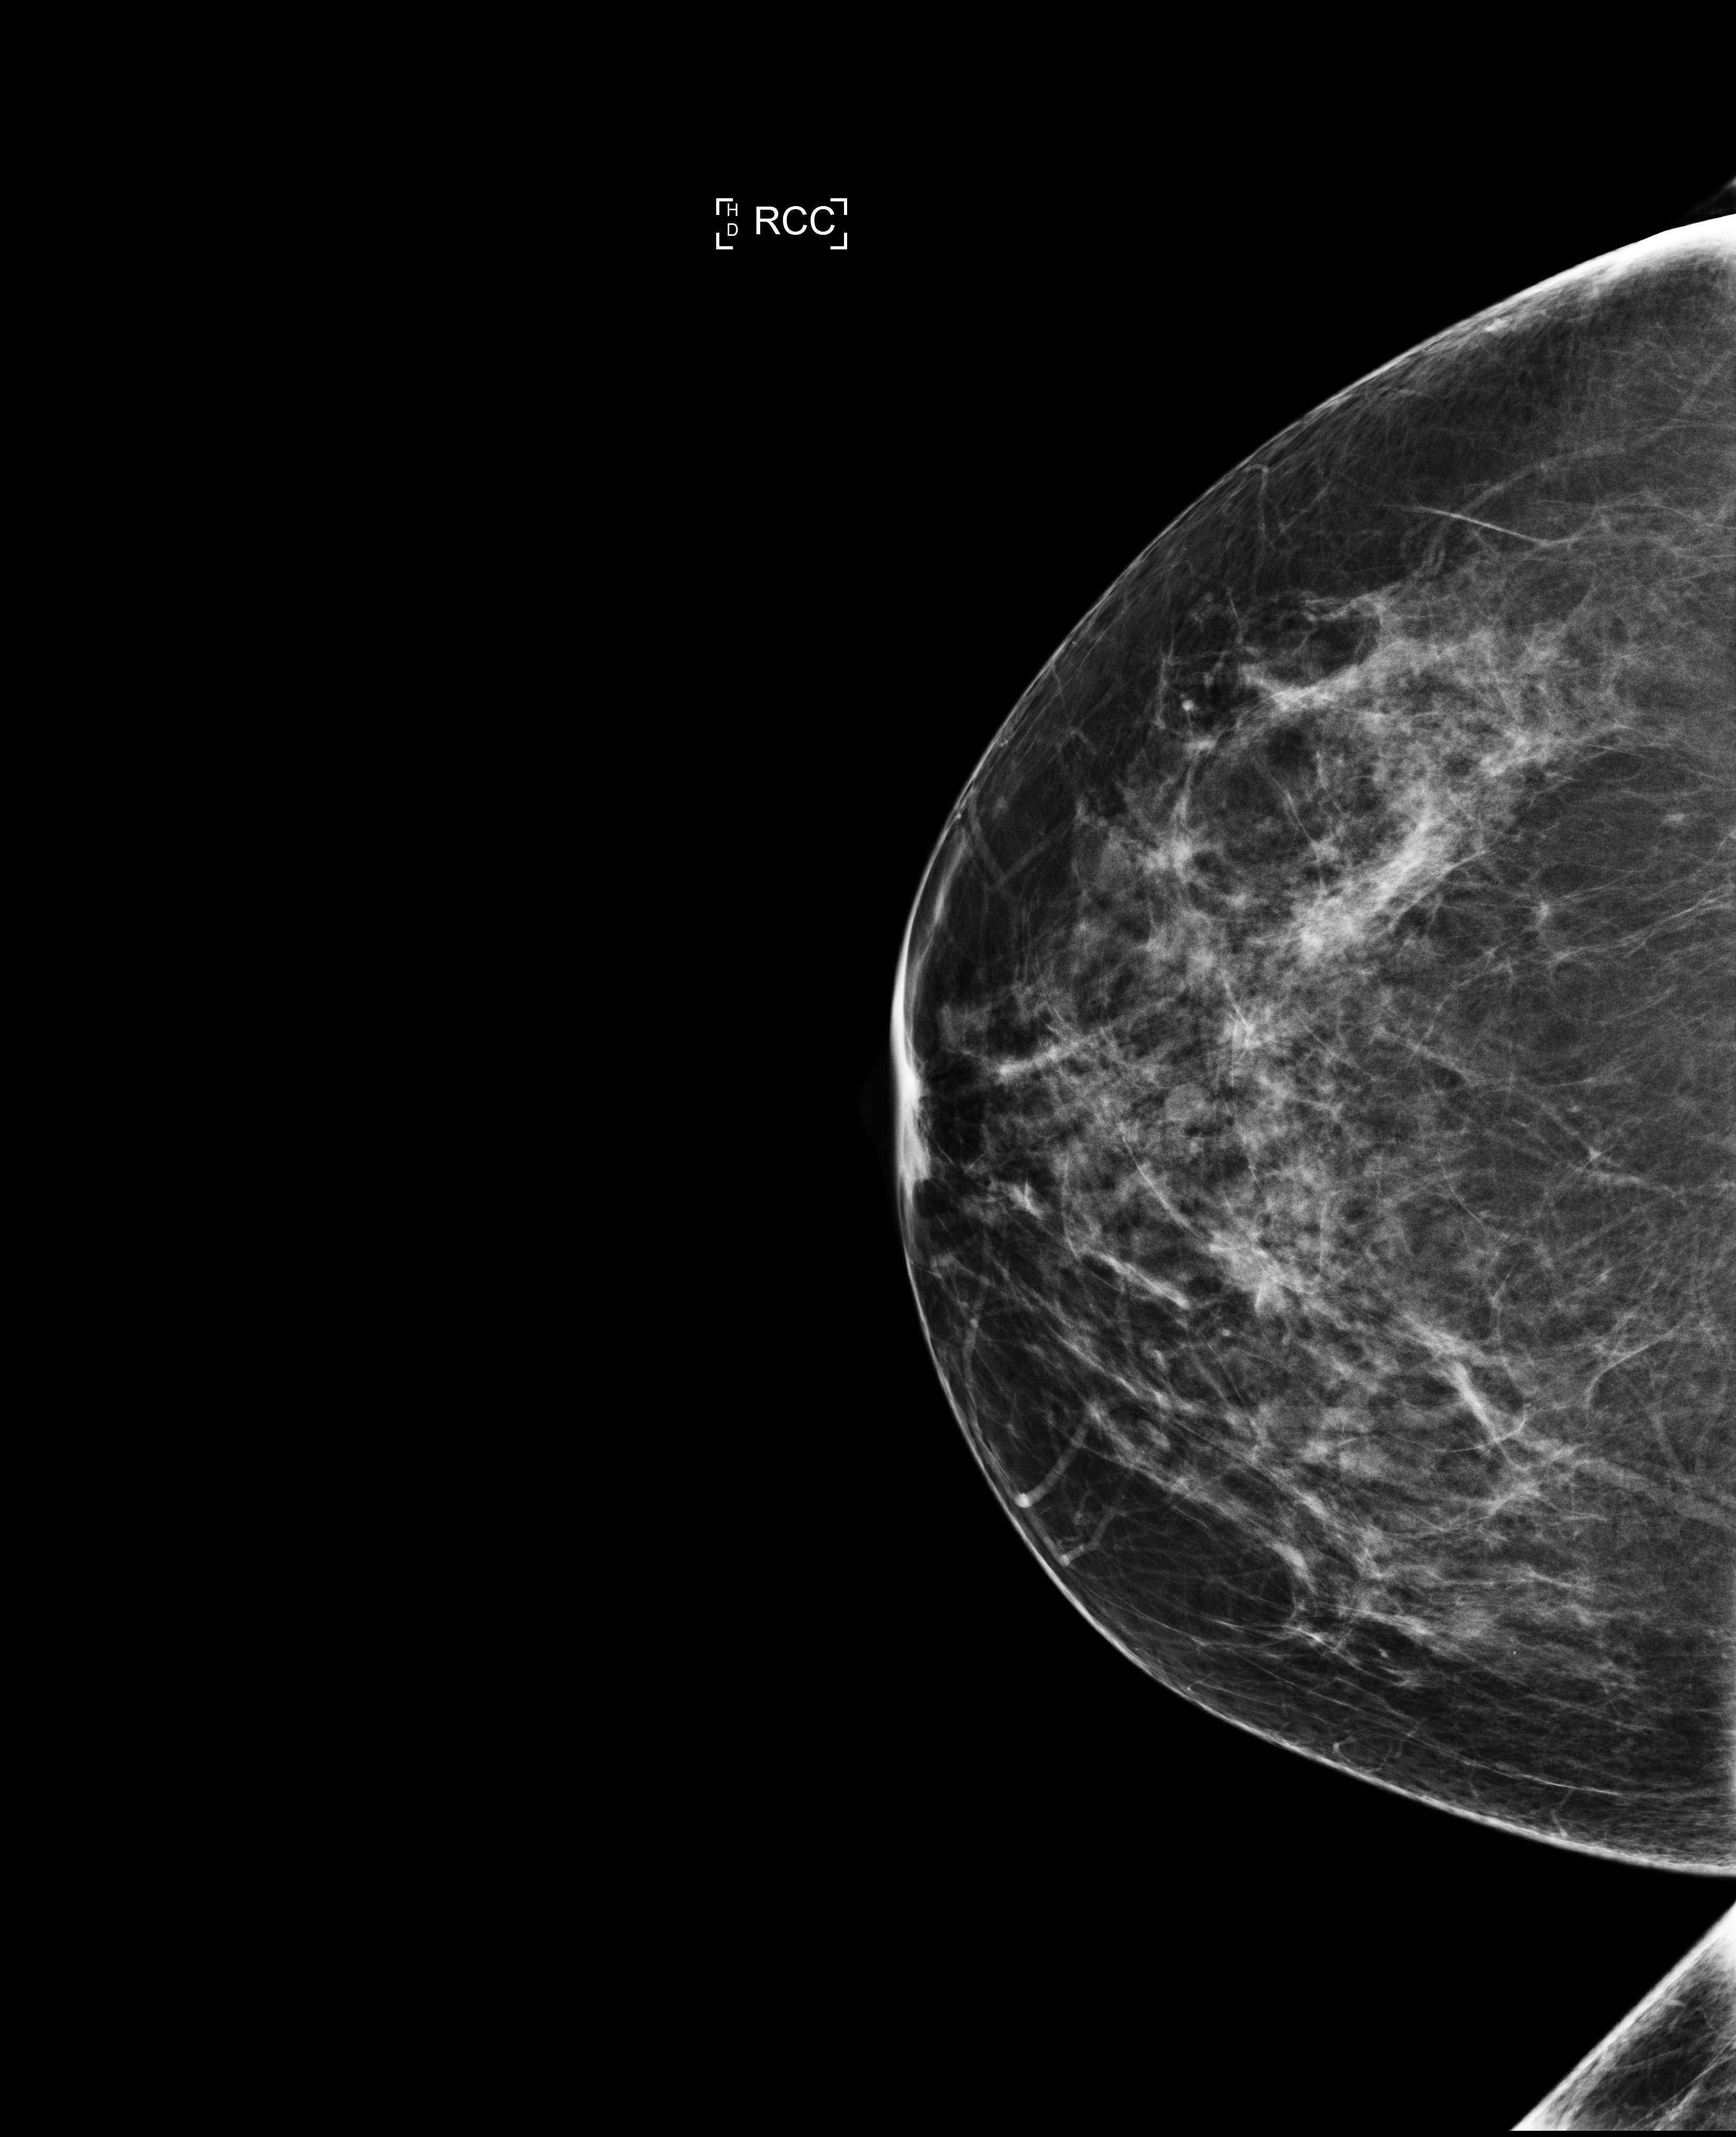
Annual screening mammography examination; compressed breast thickness 64 mm; system: Selenia Dimensions. Female patient, age 51 years.
Image type: full-field digital mammogram. Breast: right. Projection: craniocaudal (CC) view.